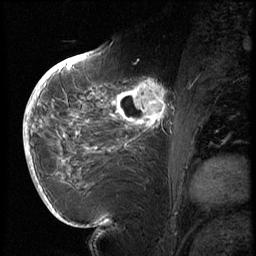
Breast MRI (dynamic contrast-enhanced), one sagittal slice. Position 29 of 72 along the scan axis. 3 images stored at this slice position (order not interpretable as contrast timing). 1.5 T. TE 4.2 ms, TR 8.9 ms. 2.5 mm slice thickness. 256 × 256 image matrix, field of view 200 × 200 mm. Patient: female, 56 years. From the clinical record (not read from this slice): setting: breast cancer imaged before/during neoadjuvant chemotherapy.
Annotated regions visible in this slice (semi-automatically segmented with operator editing):
- analysis volume of interest (the breast-tissue region the enhancement analysis was run in; not a lesion): bounding box [x1, y1, x2, y2] px = [114, 76, 177, 138]
- tumour enhancement mask (voxels above the 140 % enhancement threshold inside the analysis volume of interest): [117, 78, 170, 129]